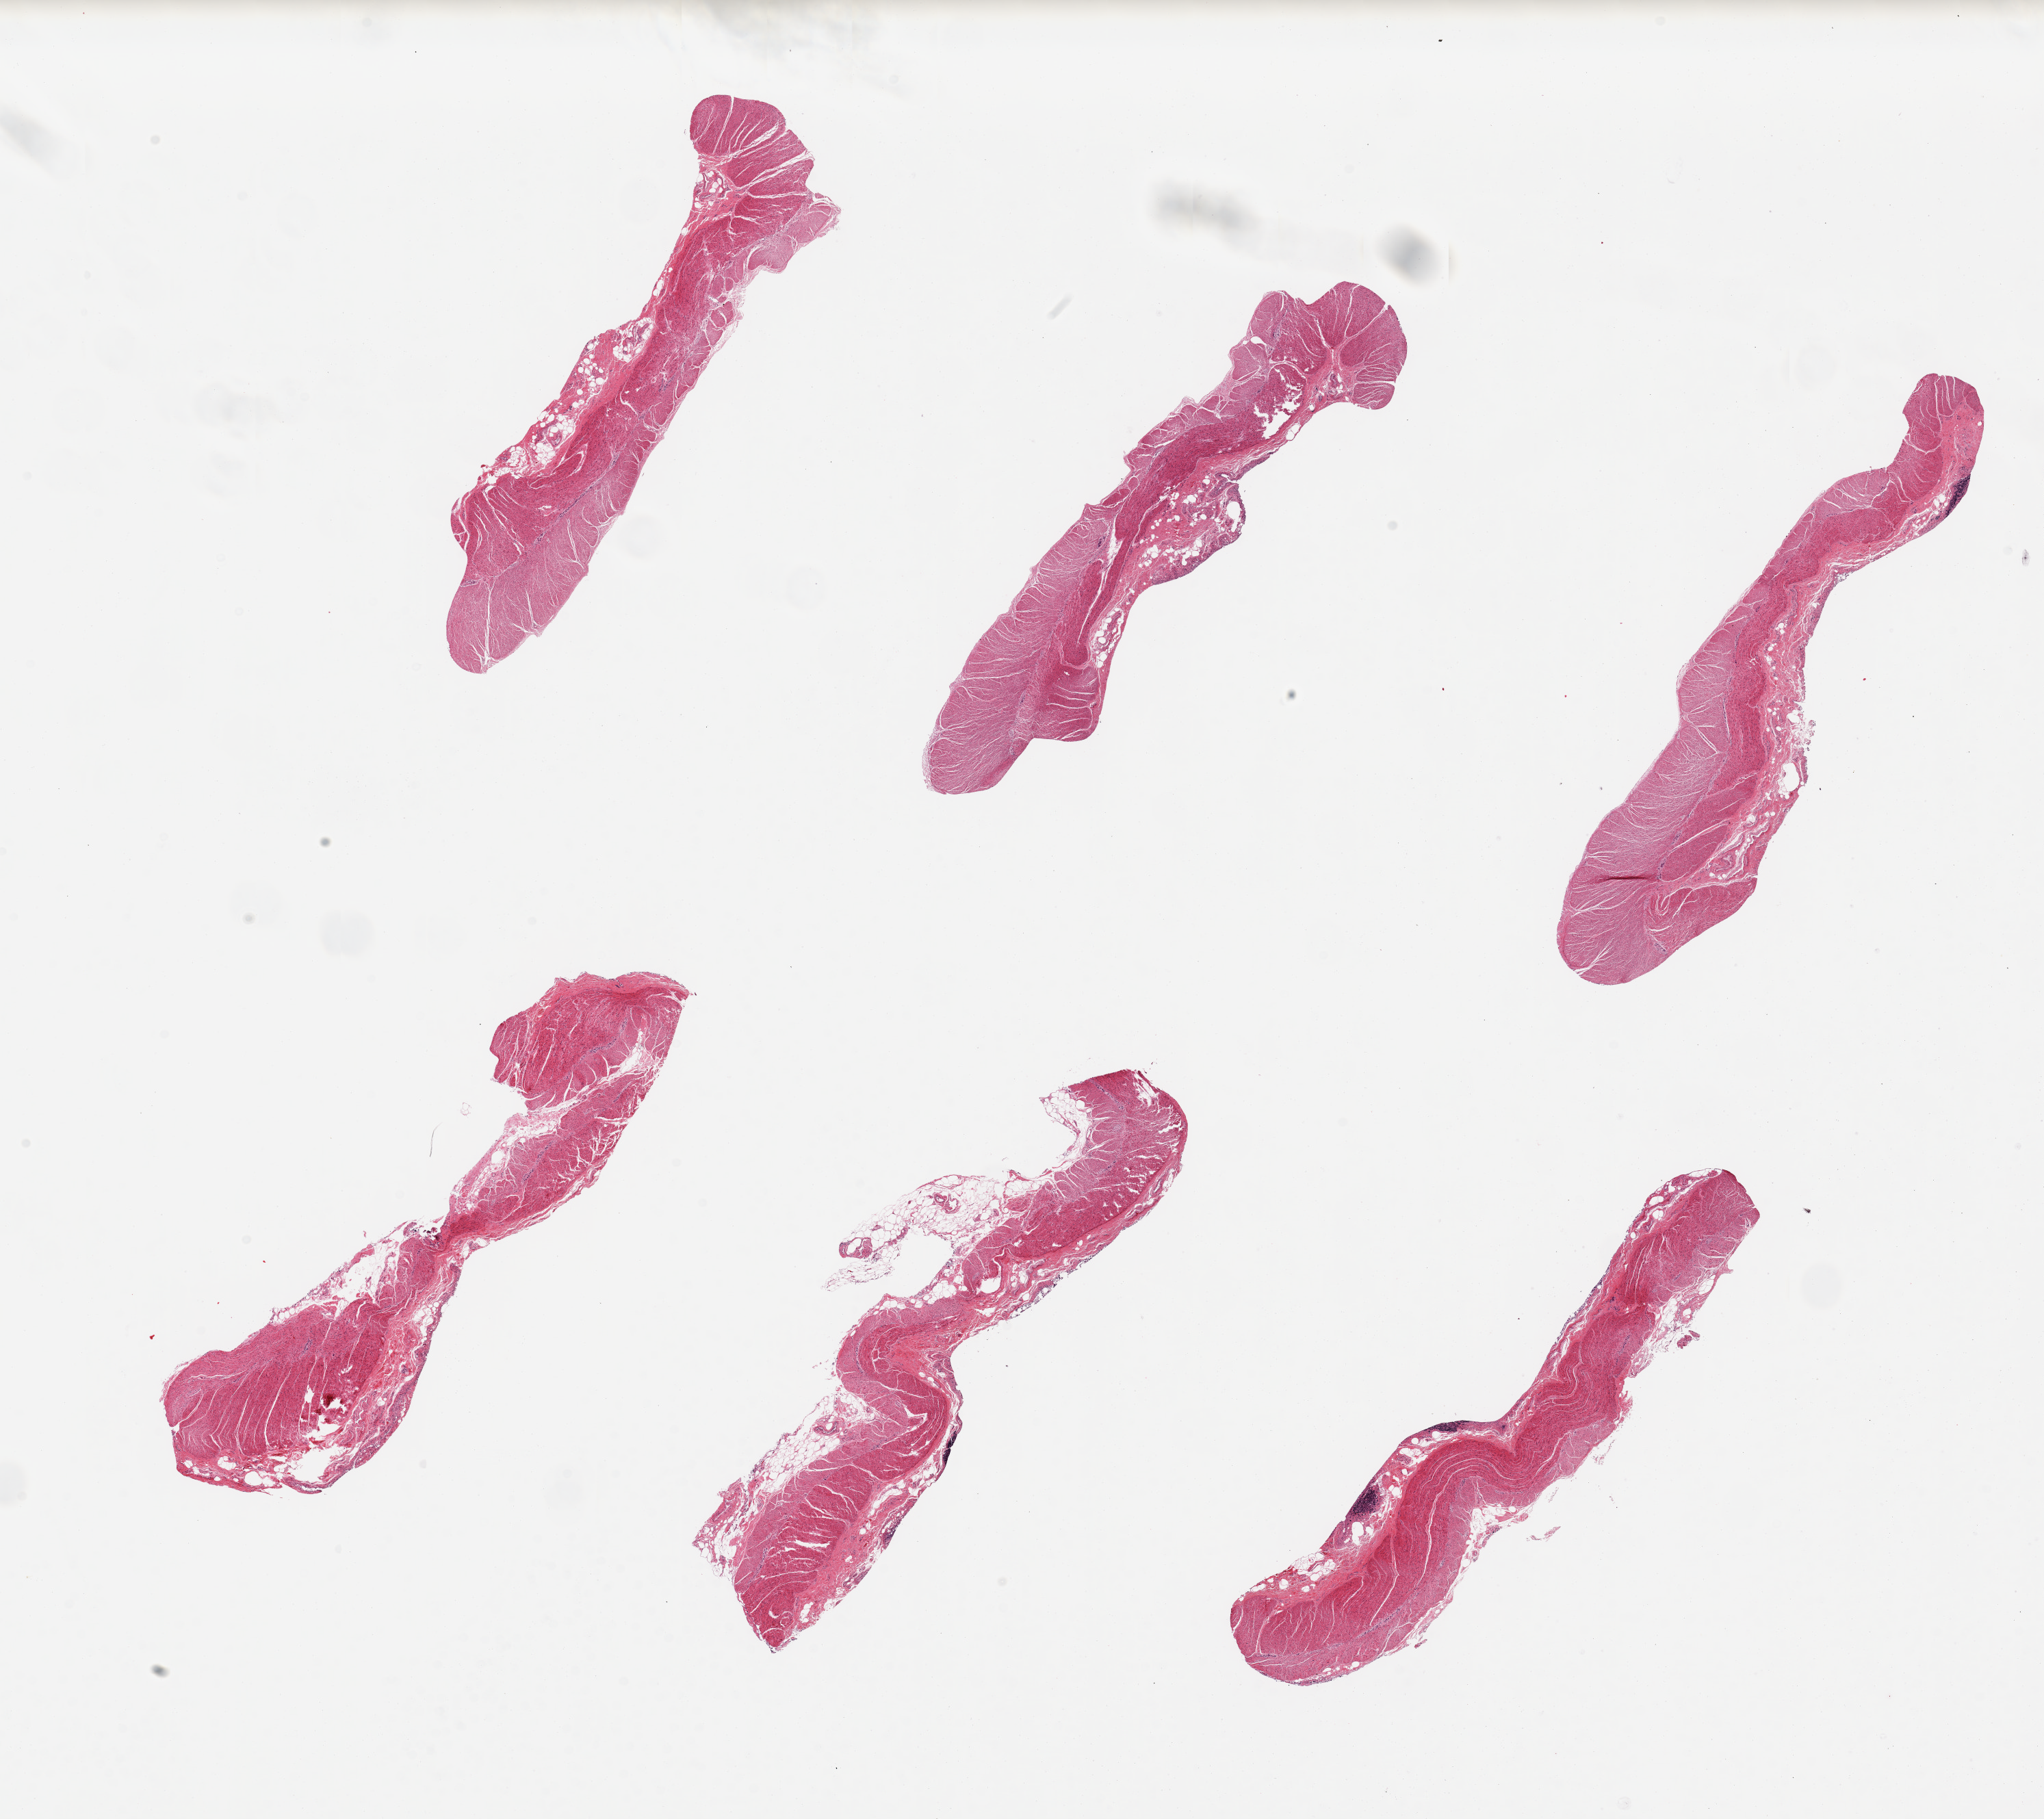
H&E whole-slide image — a low-resolution overview of the entire scanned area, about 23.6 x 21.0 mm, PAXgene-fixed paraffin-embedded (PFPE) section, target tissue: sigmoid colon, tissue donor sample.
• pathologist's review note for this sample: 6 pieces, all muscularis, trace adherent fat